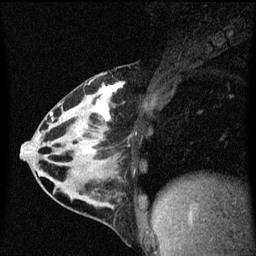
Breast MRI (dynamic contrast-enhanced), one sagittal slice. Slice 28 of 60 in the series (ordered by position). Dynamic contrast-enhanced series, image 2 of 3 at this slice position (ordered by acquisition). 1.5 T. TE 4.2 ms, TR 8.4 ms. 2 mm slice thickness. 256 × 256 image matrix. Female patient, age 32 years.
Annotated regions visible in this slice (semi-automatic segmentation, software-assisted and operator-edited):
- analysis volume of interest (the breast-tissue region the enhancement analysis was run in; not a lesion): bounding box <34,74,143,169> (left, top, right, bottom; pixels)
- tumour enhancement mask (voxels above the 70 % enhancement threshold inside the analysis volume of interest): <51,82,125,153>